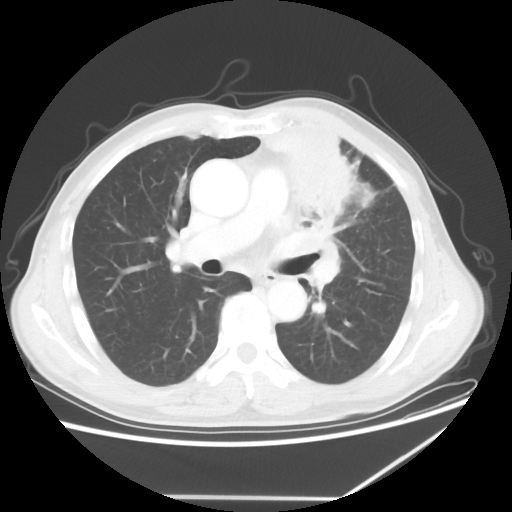
Chest CT, one axial slice; position 36 of 64 along the scan axis; reconstruction kernel STANDARD; lung window (W 1500 / L -600 HU); 512 × 512 image matrix, field of view 383 × 383 mm. Male patient, age 64 years. Case-level facts recorded for this patient, not image findings: clinical TNM (as recorded): T1c N1 M1; histopathological grade: G2.
Structures marked on this image (bounding box drawn by a radiologist):
- lung tumour (recorded histology: squamous cell carcinoma): bounding box <263,109,388,285> (left, top, right, bottom; pixels)